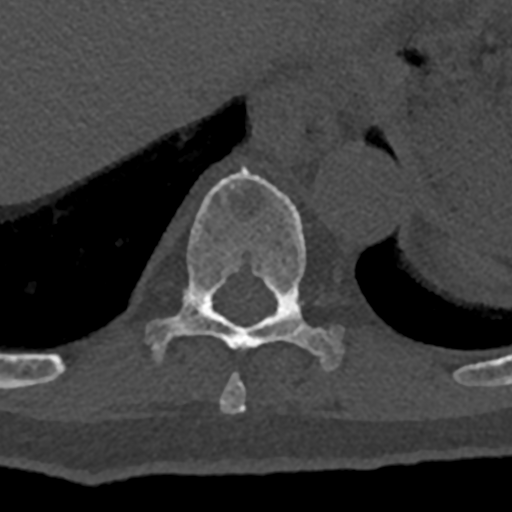
CT including the spine, one axial slice. Slice 603 of 797 in the series (ordered by position). 120 kVp. Bone window (W 1800 / L 400 HU). 512 × 512 image matrix, field of view 160 × 160 mm. Patient: male, 74 years. From the clinical record (not read from this slice): primary cancer: renal; vertebrae with lytic lesions (as recorded): T10, L1, L2, L3, L4, L5.
Outlined on this slice (semi-automatic segmentation, software-assisted and operator-edited):
- T10 vertebra: box from (x=147, y=164) to (x=342, y=371) px
- T9 vertebra: (x=219, y=373)–(x=247, y=413)